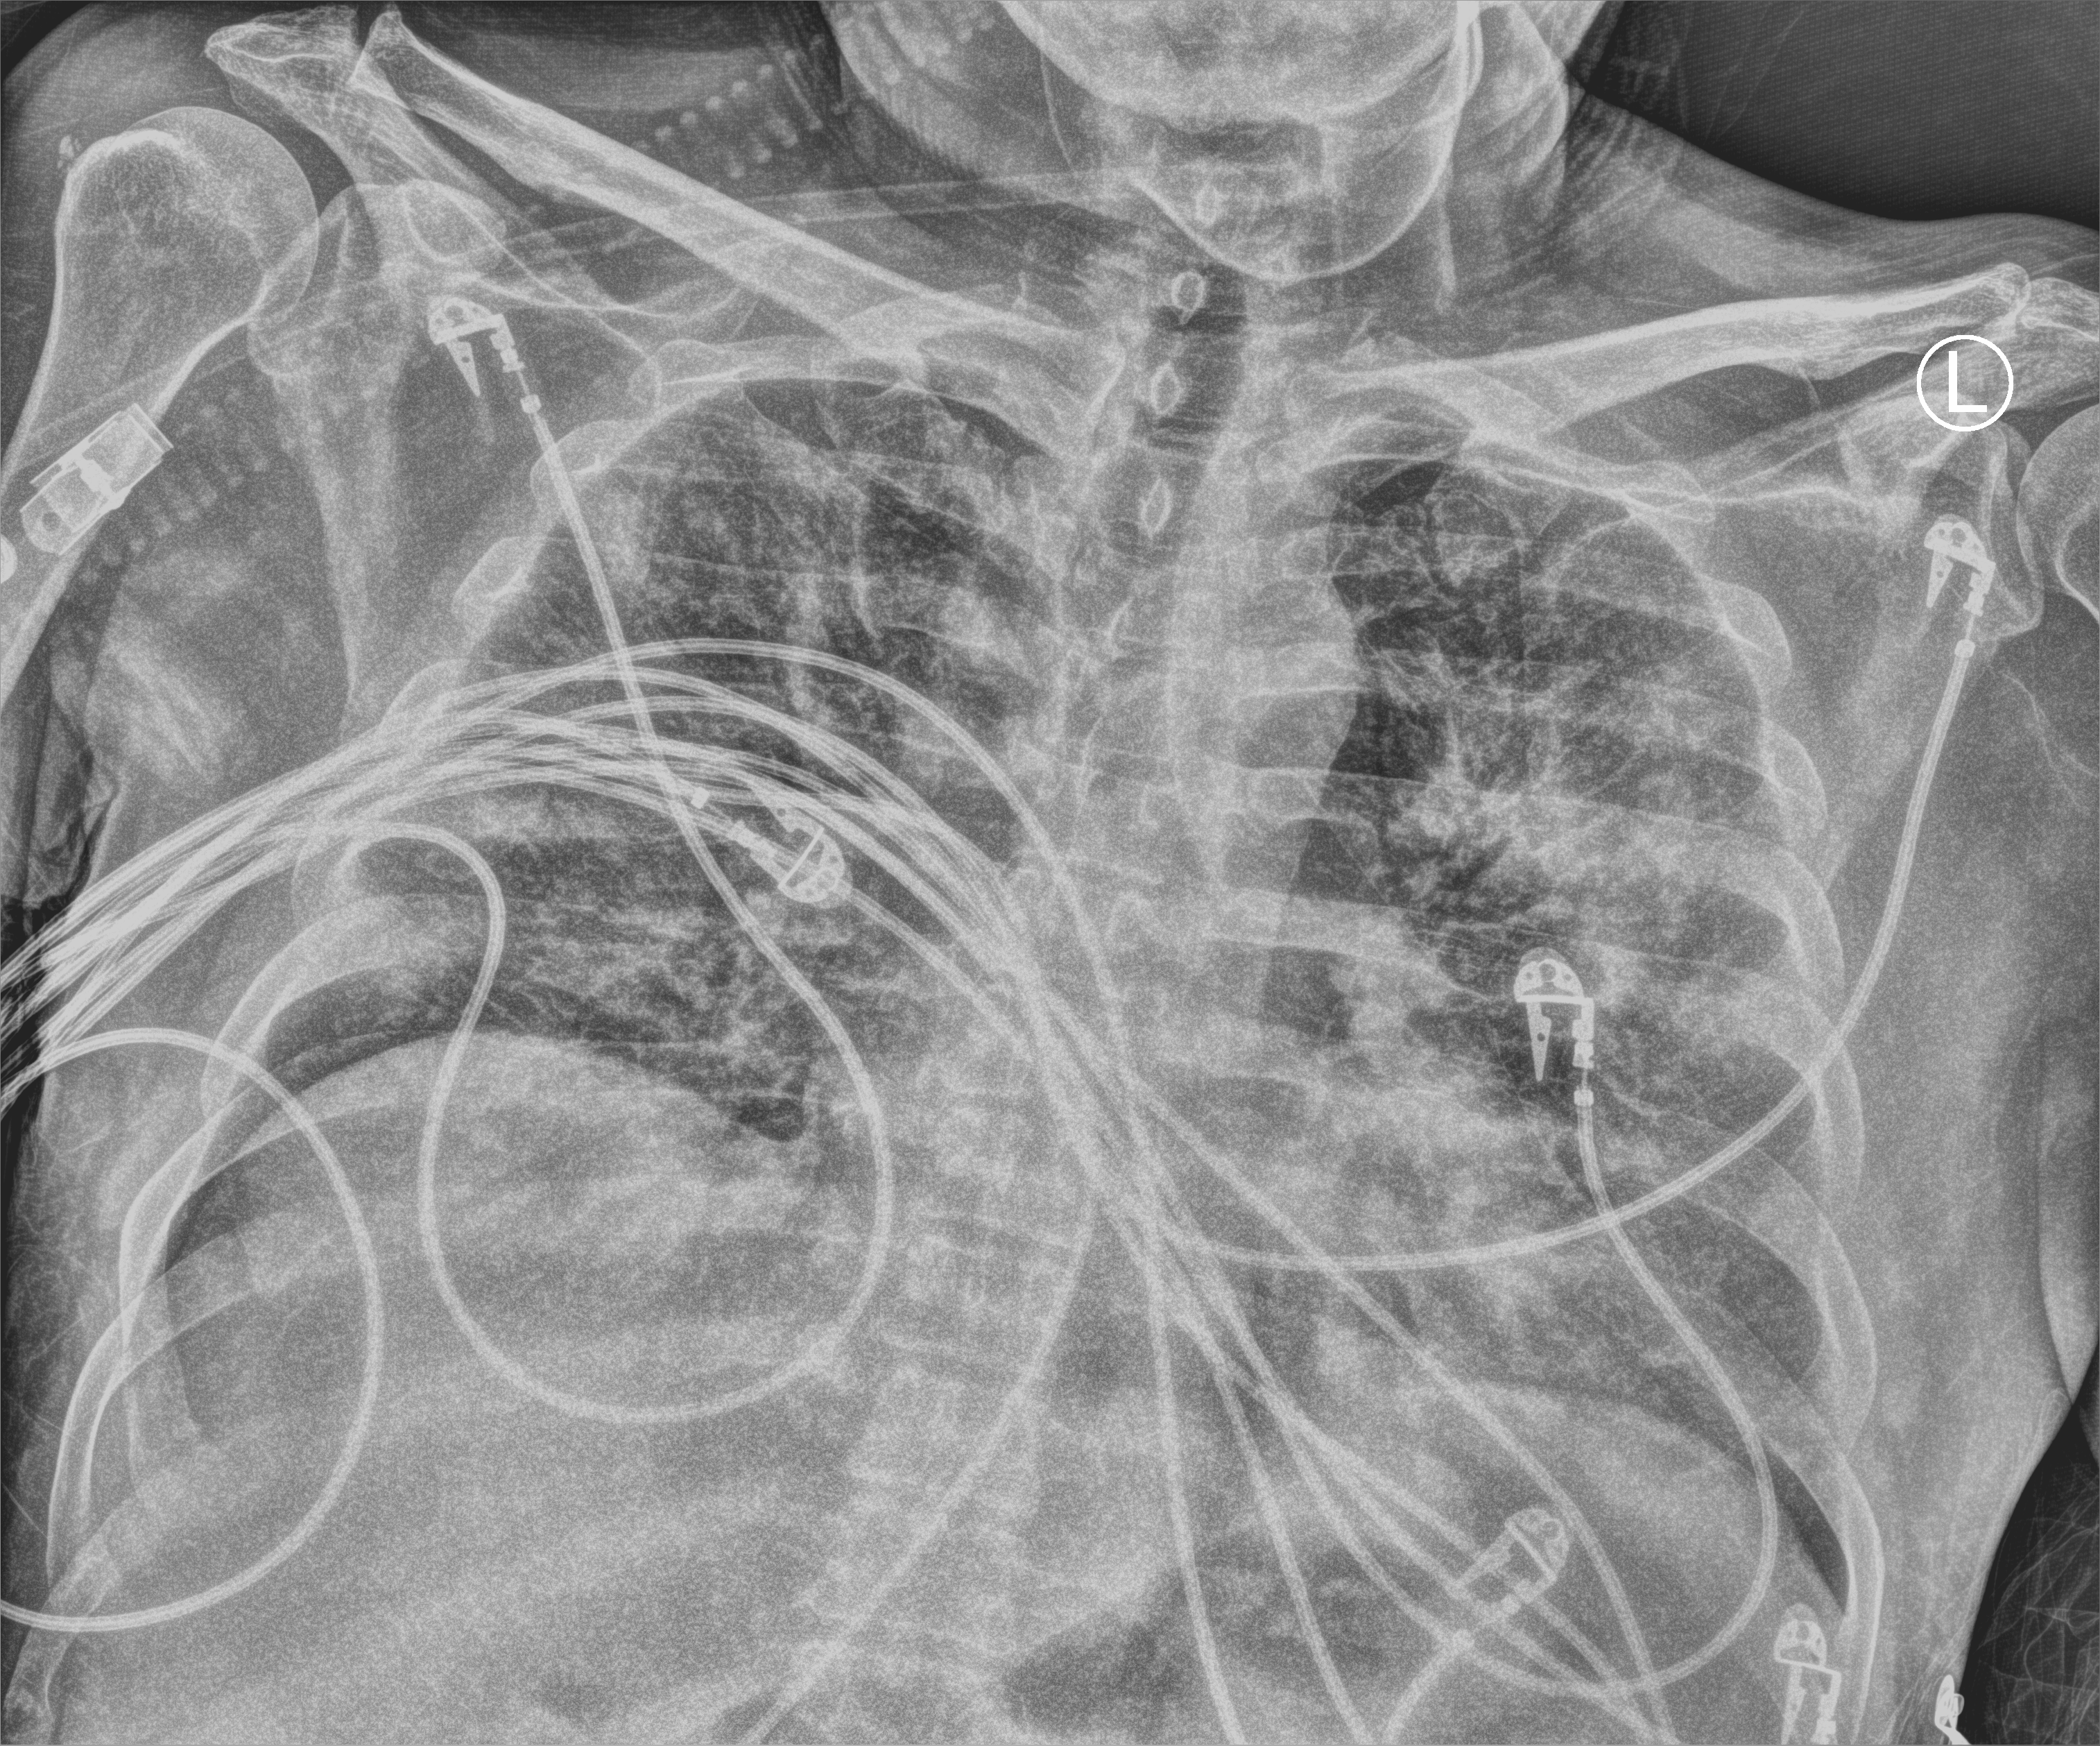
Bedside chest radiograph (computed radiography), anteroposterior (AP) projection. Male patient hospitalised with COVID-19, age 18–59 years.
Admission-level facts for this patient (not findings on this image; timing relative to this image not recorded):
- admitted to intensive care during this hospital stay: yes
- mechanically ventilated during this hospital stay: yes